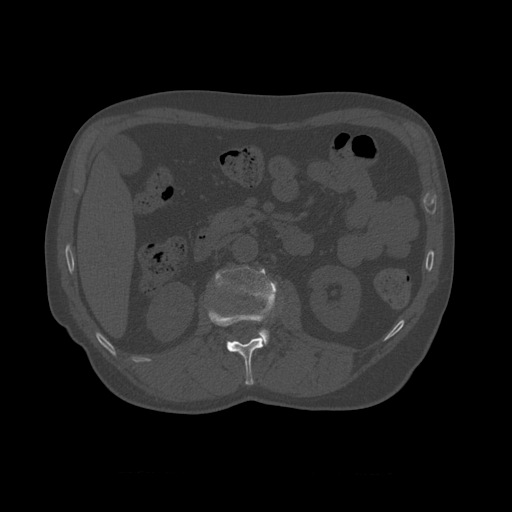
CT including the spine, one axial slice; position 347 of 450 along the scan axis; bone window (W 1800 / L 400 HU); 512 × 512 image matrix, field of view 405 × 405 mm. Patient age 75 years. Case-level facts recorded for this patient, not image findings: primary cancer: prostate.
Outlined on this slice (semi-automatically segmented with operator editing):
- L1 vertebra: bounding box [x1, y1, x2, y2] px = [208, 287, 277, 386]
- L2 vertebra: [213, 266, 279, 345]